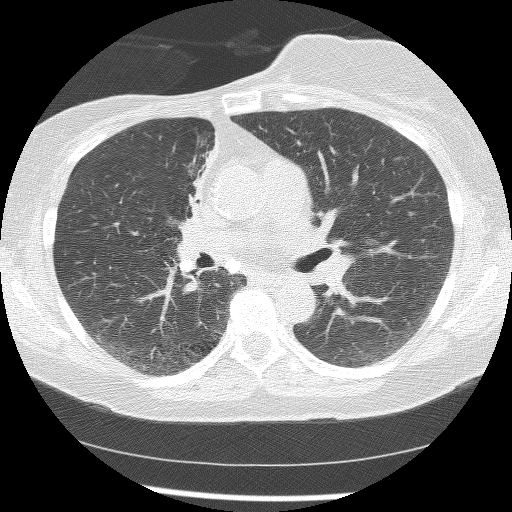
Chest CT (low-dose screening protocol), one axial image, baseline annual screen, lung window (W 1500 / L -600 HU), 2.5 mm slice thickness, slice 68 of 172 in the series. Female, age 56 years at enrolment.
- Expert-annotated lung lesion, bounding box <160,130,214,252> (left, top, right, bottom; pixels).
- The screening reader recorded 2 non-calcified nodules or masses ≥4 mm on this exam (right lower lobe, right middle lobe); which of them this box marks is not recorded.
- Official screen result: positive, change unspecified: nodule(s) >= 4 mm or enlarging nodule(s), mass(es), or other non-specific abnormalities suspicious for lung cancer.
- Later outcome: lung cancer diagnosed 1185 days after this screen — adenocarcinoma, NOS, right upper lobe, stage IIIB (AJCC 6th edition), 8 mm at pathology.